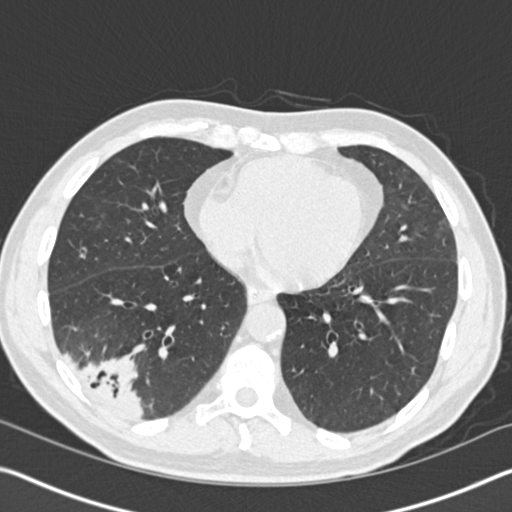
Chest CT (low-dose screening protocol), one axial image; first (baseline) screen; lung window (W 1500 / L -600 HU); slice 101 of 161 in the series; 512 × 512 image matrix, field of view 340 × 340 mm. Male participant, aged 61 years at enrolment. Current smoker at enrolment.
• Expert-annotated lung lesion, bounding box (x1, y1, x2, y2) in pixels: (40, 315, 153, 421).
• Screening reader's record for this exam (one nodule recorded; not confirmed to be the boxed lesion): non-calcified nodule or mass ≥4 mm, right lower lobe, 52 × 36 mm, spiculated (stellate) margins, soft tissue attenuation.
• Official screen result: positive, change unspecified: nodule(s) >= 4 mm or enlarging nodule(s), mass(es), or other non-specific abnormalities suspicious for lung cancer.